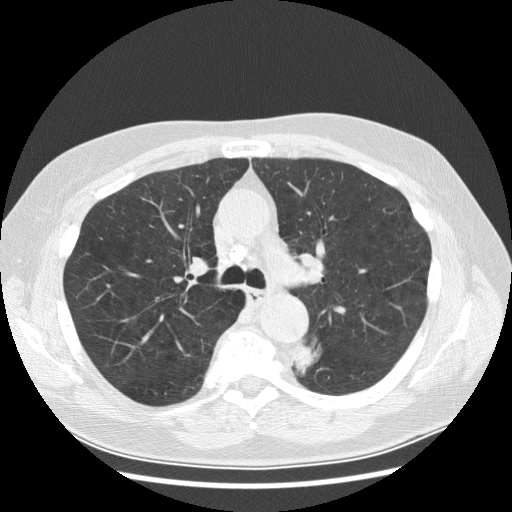
Low-dose screening chest CT, axial slice. Baseline annual screen. Lung window (W 1500 / L -600 HU). Standard (soft-tissue) reconstruction kernel (STANDARD). Male, age 70 years at enrolment. Current smoker at enrolment.
- Expert reader's lesion annotation, box from (x=277, y=337) to (x=325, y=379) px.
- Reader record for this screening exam (exam-level; its link to the box is not recorded): non-calcified nodule or mass ≥4 mm, left lower lobe, 27 × 16 mm, spiculated (stellate) margins, soft tissue attenuation, pre-existing on the prior screen: yes; interval growth: yes.
- Official screen result: positive, change unspecified: nodule(s) >= 4 mm or enlarging nodule(s), mass(es), or other non-specific abnormalities suspicious for lung cancer.
- Participant outcome: lung cancer diagnosed 97 days after this screen — papillary adenocarcinoma, NOS, left lower lobe, moderately differentiated (G2), stage IB (AJCC 6th edition), 35 mm at pathology.